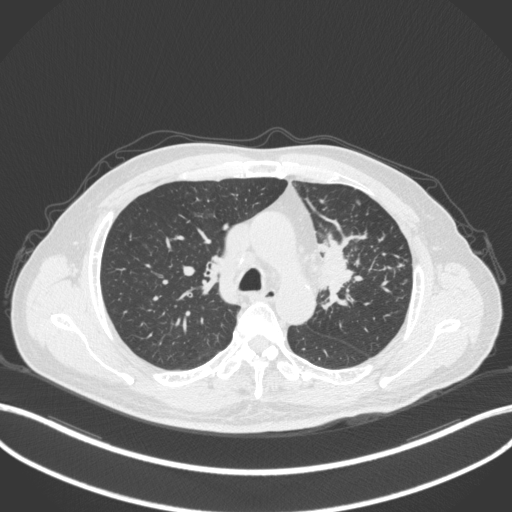
Chest CT, one axial slice; position 240 of 386 along the scan axis; reconstruction kernel B31f; lung window (W 1500 / L -600 HU); 1 mm slice thickness; 512 × 512 image matrix, field of view 400 × 400 mm. Male patient, age 69 years. From the clinical record (not read from this slice): clinical TNM (as recorded): T2a N2 M0.
Annotated regions visible in this slice (bounding box drawn by a radiologist):
- lung tumour (recorded histology: adenocarcinoma): bounding box (x1, y1, x2, y2) in pixels: (319, 227, 369, 322)